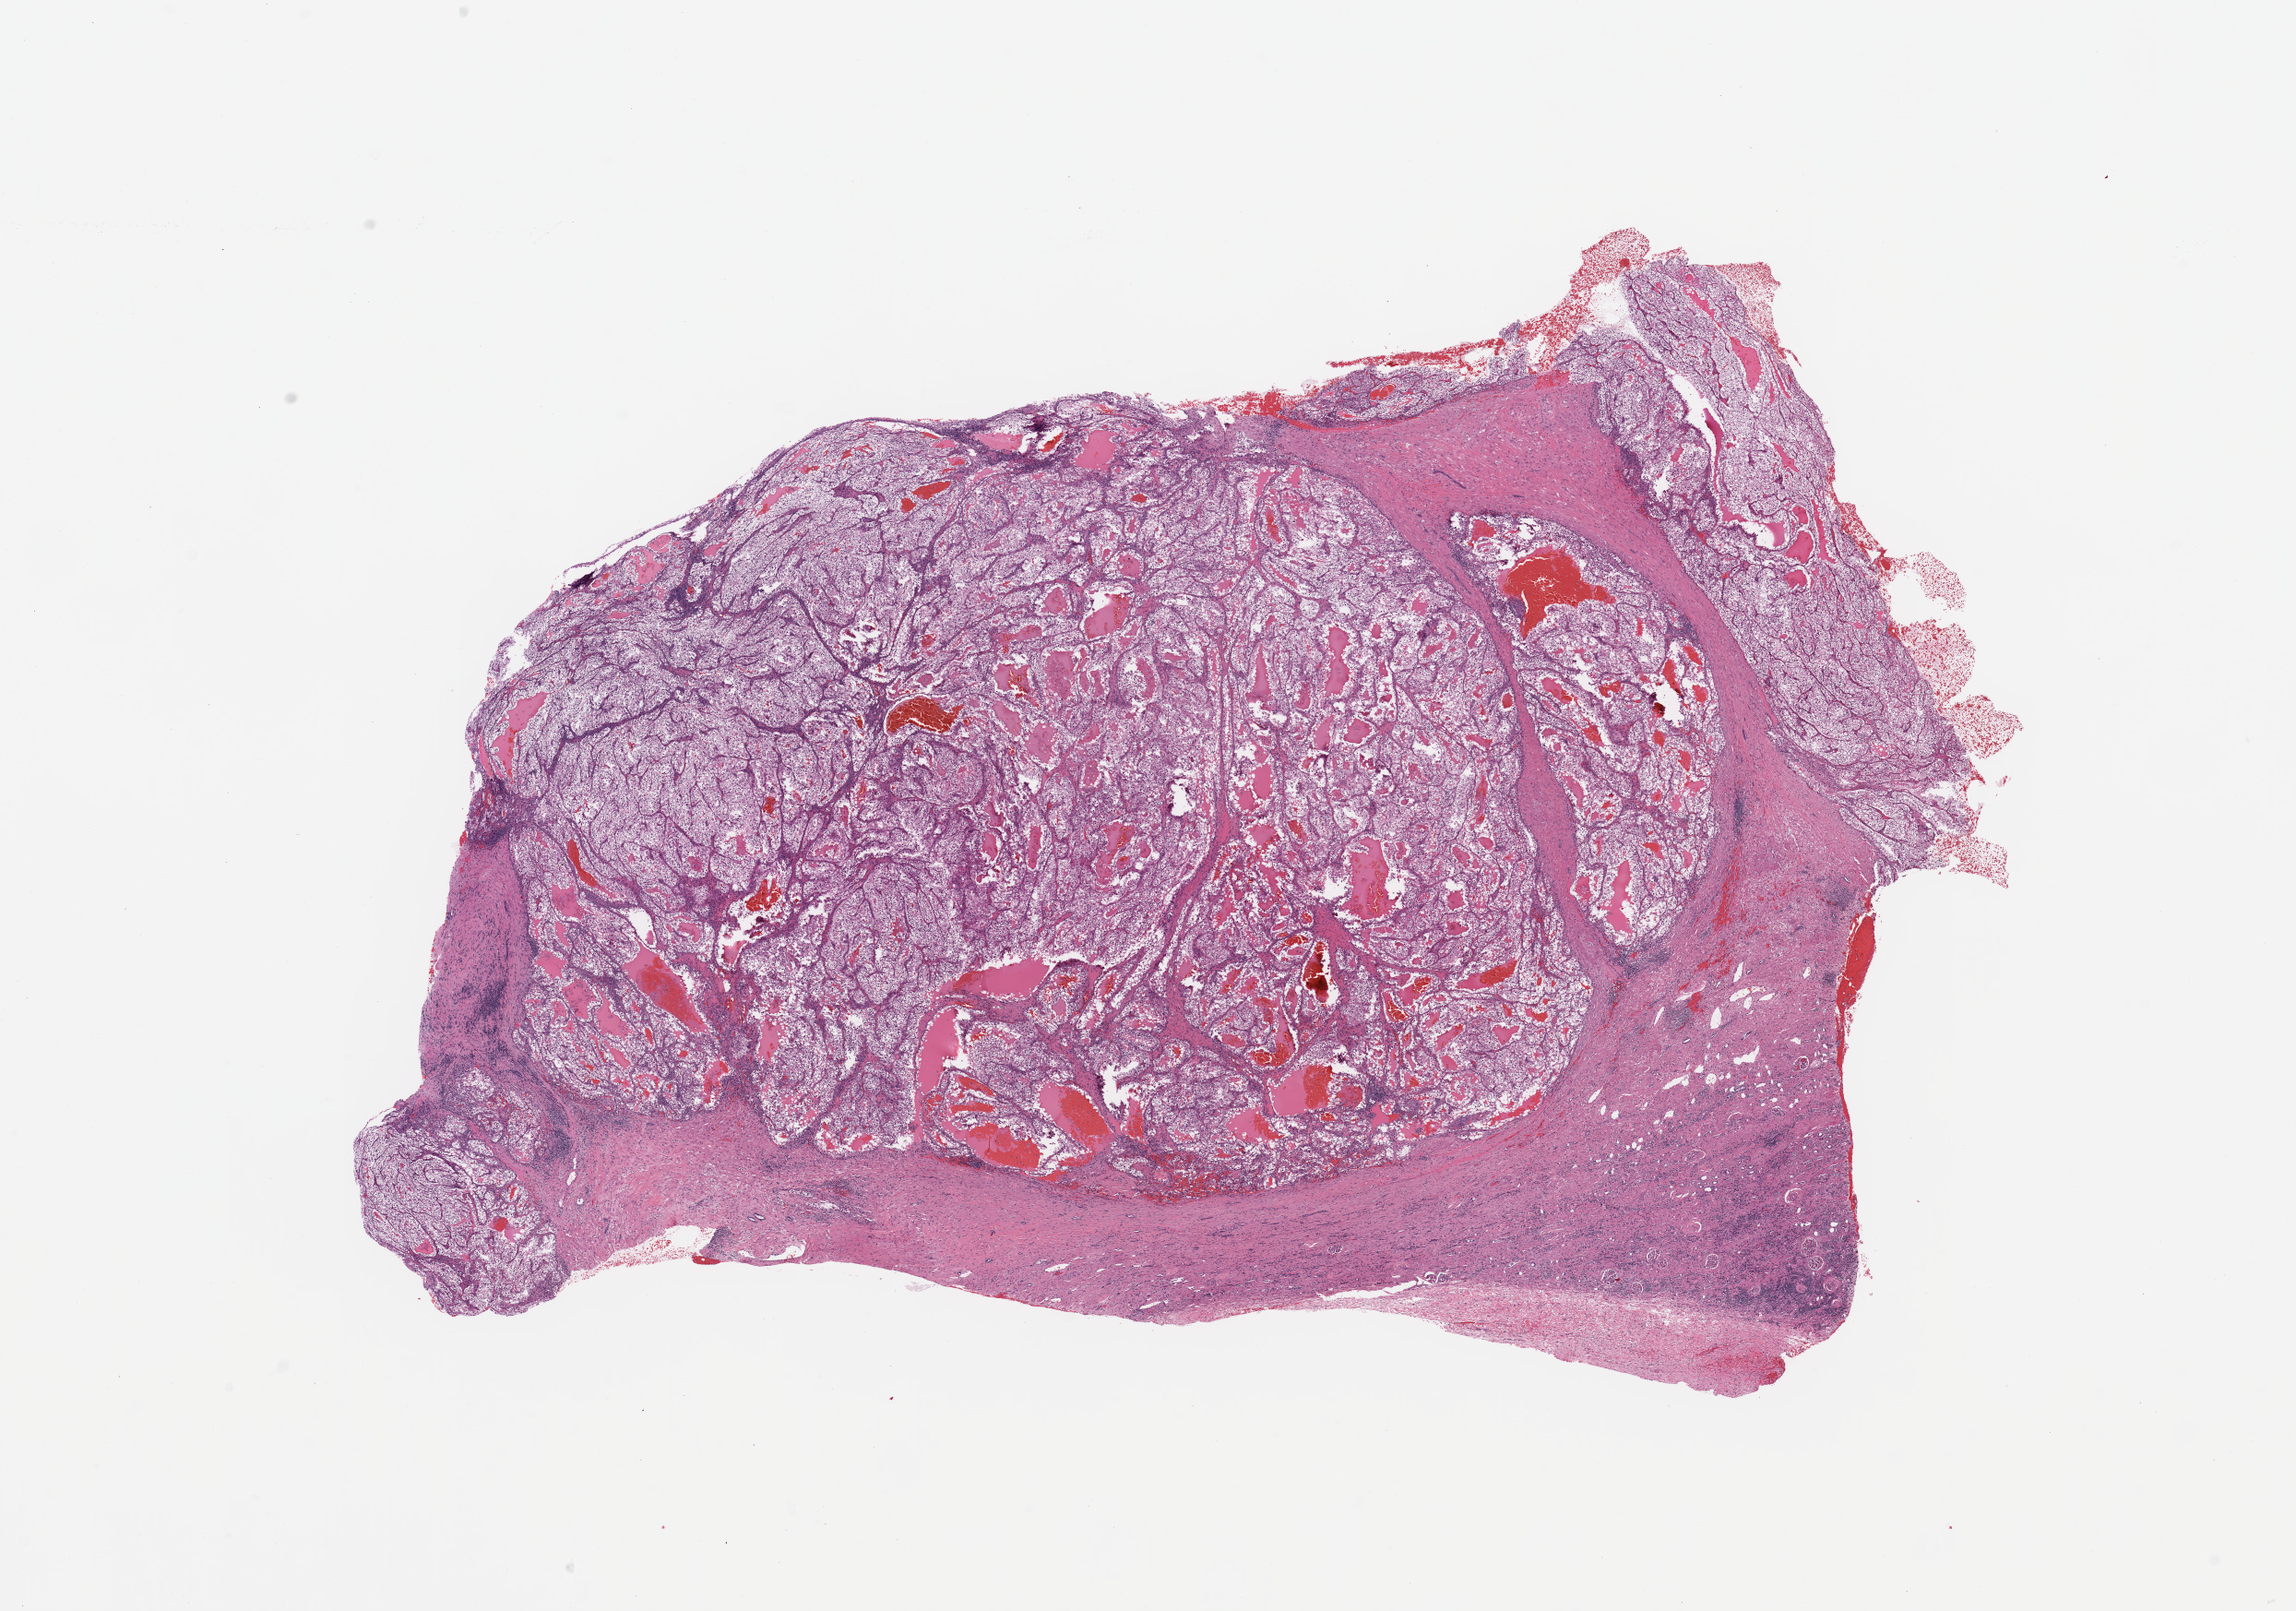
Whole-slide histology image, H&E — shown as a low-resolution overview of the whole scanned area (about 19.7 x 13.8 mm), kidney, tumour tissue. Patient: male, age 55 years. Histologic grade: G3 (poorly differentiated).
- AJCC pathologic stage: IV
- diagnosis: Renal cell carcinoma, NOS